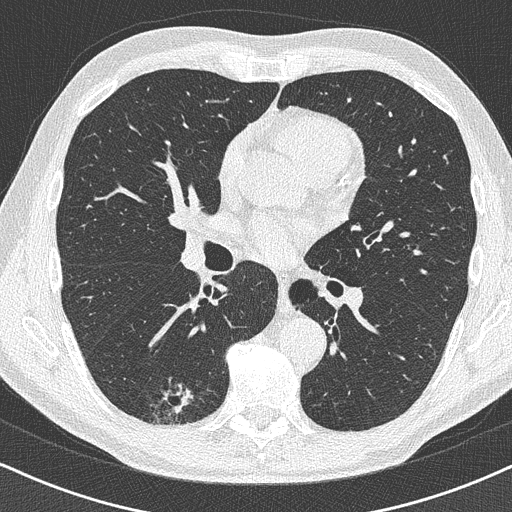
Low-dose screening chest CT, one axial slice; position 232 of 438 along the scan axis; lung window (W 1500 / L -600 HU); 1 mm slice thickness; 512 × 512 image matrix, field of view 320 × 320 mm.
Structures marked on this image (outlined manually by an expert reader):
- lesion 1 (tumor, lower lobe of right lung): bounding box <174,388,192,413> (left, top, right, bottom; pixels)